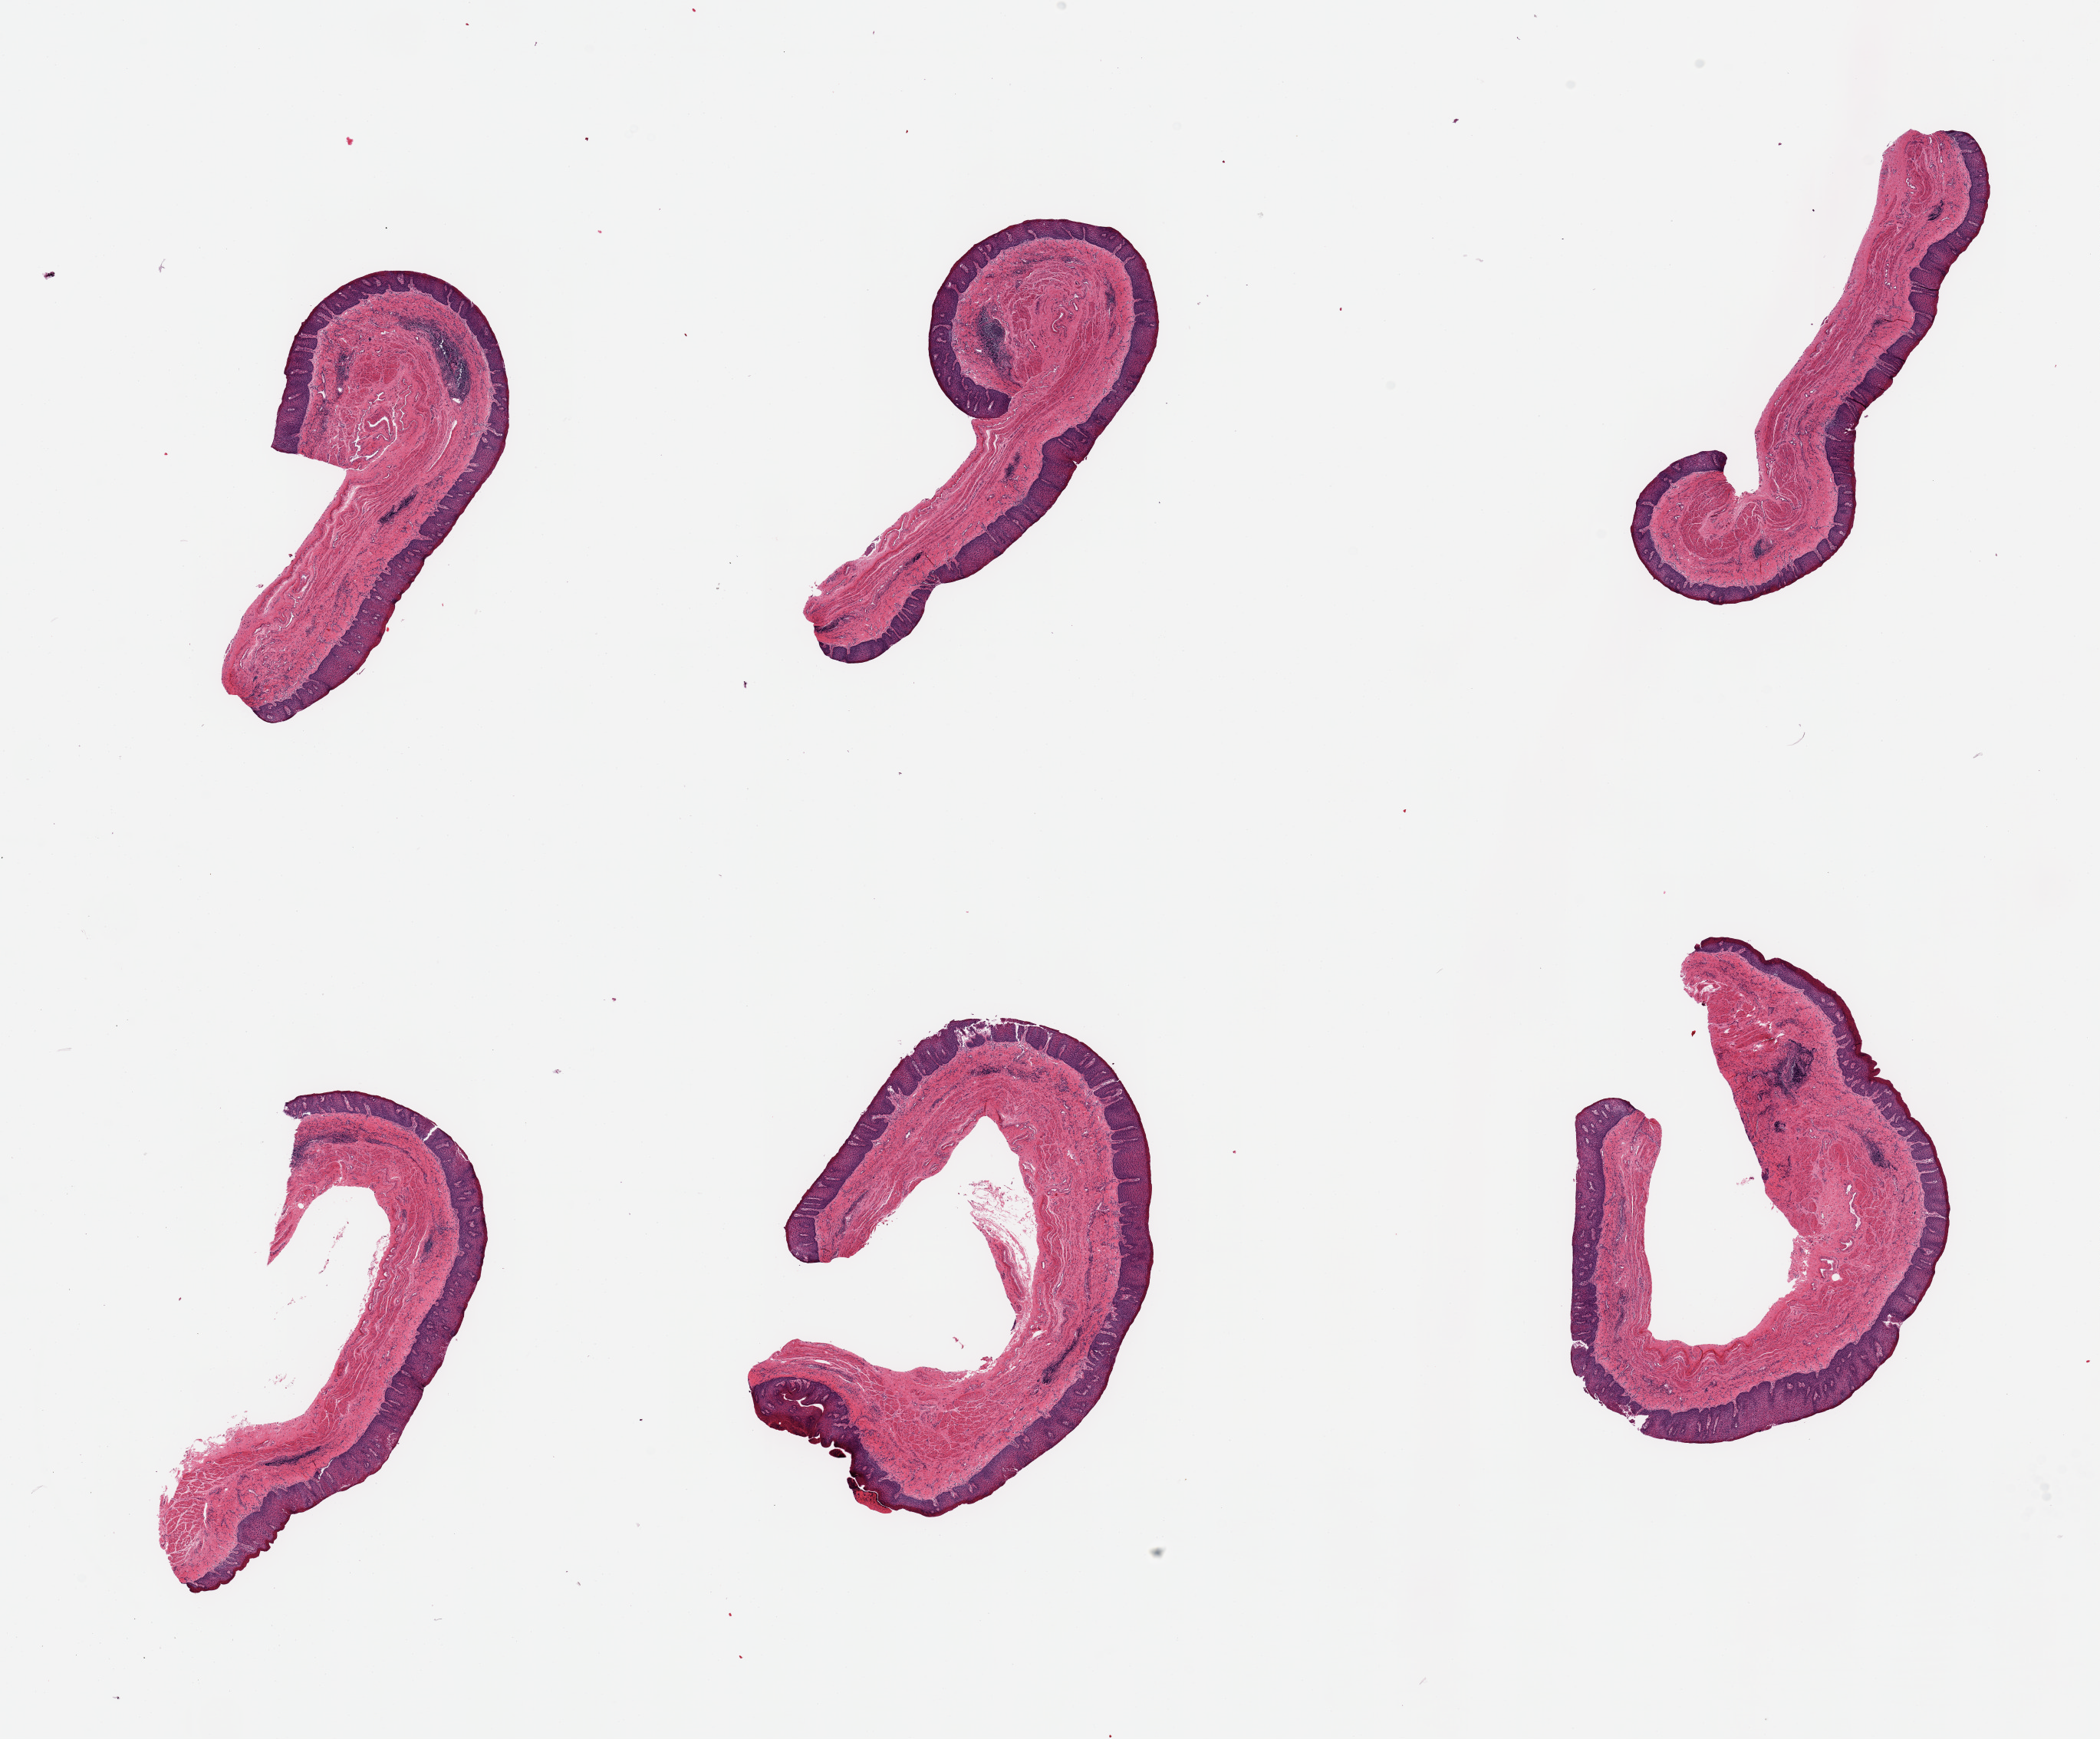
Whole-slide image, hematoxylin and eosin (H&E) stain — a low-resolution overview of the entire scanned area, about 21.7 x 17.9 mm; PAXgene-fixed, paraffin-embedded tissue; target tissue: esophageal mucous membrane; donor tissue sample. Male donor.
- reviewer comment on this tissue sample: 6 pieces, squamous mucosa is ~0.25-0.5mm, ~25% thickness